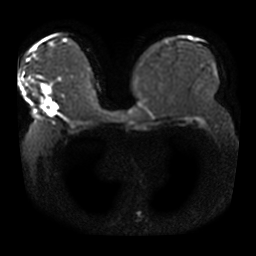
Breast MRI, one axial slice. Diffusion-weighted series; image 2 of 4 stored at this slice position (different b-values; order by instance number). 3 T. 5 mm slice thickness. 256 × 256 image matrix, field of view 360 × 360 mm. Female patient.
Outlined on this slice (manually delineated by an expert):
- tumour on diffusion-weighted imaging: bounding box (x1, y1, x2, y2) in pixels: (41, 98, 59, 117)